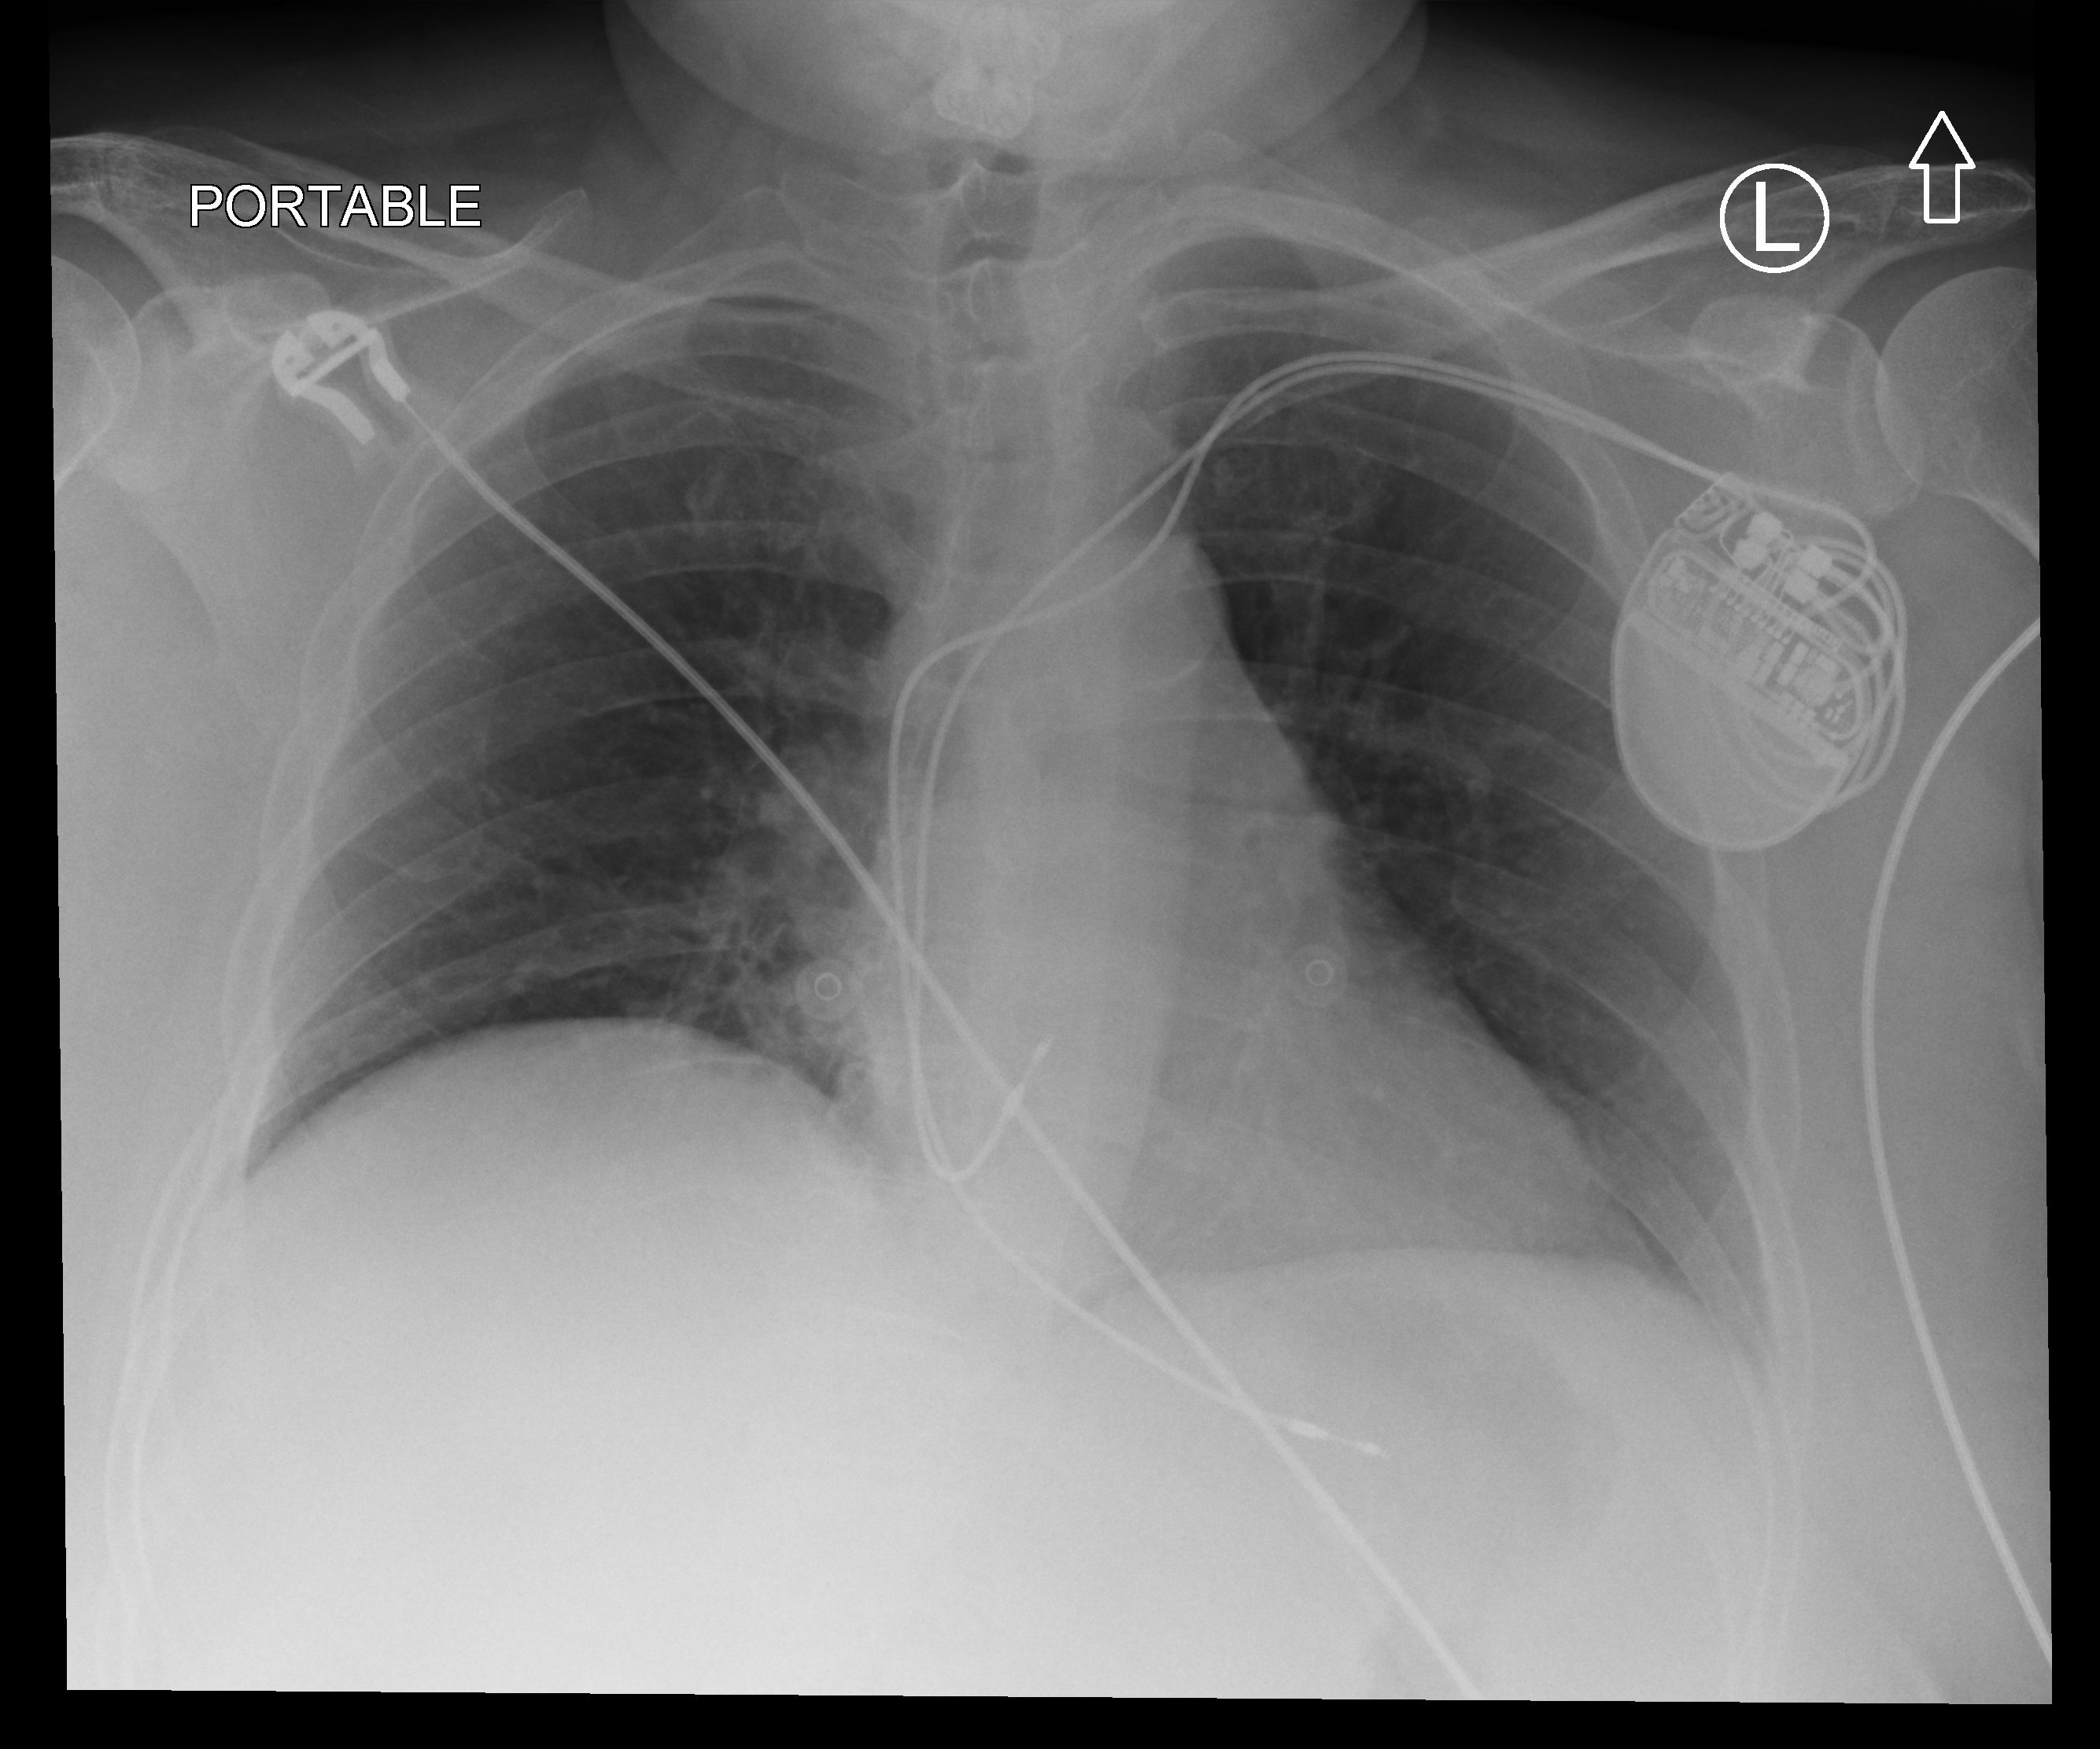
Bedside chest radiograph (computed radiography), anteroposterior (AP) projection. Patient hospitalised with COVID-19; female, aged 18–59 years.
From the hospital-stay record, not from the radiograph (when in the stay this image was taken is not recorded): mechanically ventilated during this hospital stay: no; chronic kidney disease (admission record): no.